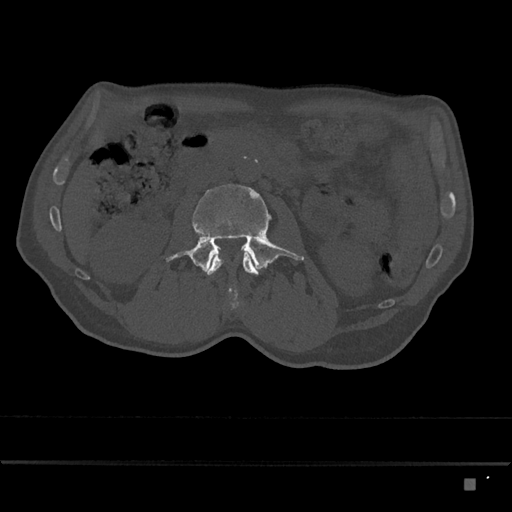
CT including the spine, one axial slice; slice 429 of 797 in the series (ordered by position); reconstruction kernel Br40s/3; 120 kVp; bone window (W 1800 / L 400 HU); 0.5 mm slice thickness; 512 × 512 image matrix, field of view 390 × 390 mm. Male patient, age 72 years. Case-level facts recorded for this patient, not image findings: primary cancer: prostate.
Outlined on this slice (semi-automatically segmented with operator editing):
- L2 vertebra: bounding box (x1, y1, x2, y2) in pixels: (204, 252, 258, 294)
- L3 vertebra: (166, 184, 304, 273)